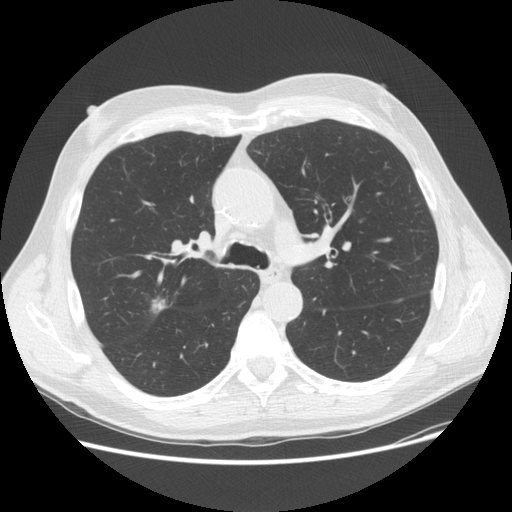
Low-dose screening chest CT, one axial slice; slice 102 of 156 in the series (ordered by position); reconstruction kernel STANDARD; 120 kVp; lung window (W 1500 / L -600 HU); 2.5 mm slice thickness; 512 × 512 image matrix, field of view 380 × 380 mm.
Annotated regions visible in this slice (expert manual segmentation):
- lesion 1 (tumor, upper lobe of right lung): bounding box (x1, y1, x2, y2) in pixels: (152, 298, 166, 313)